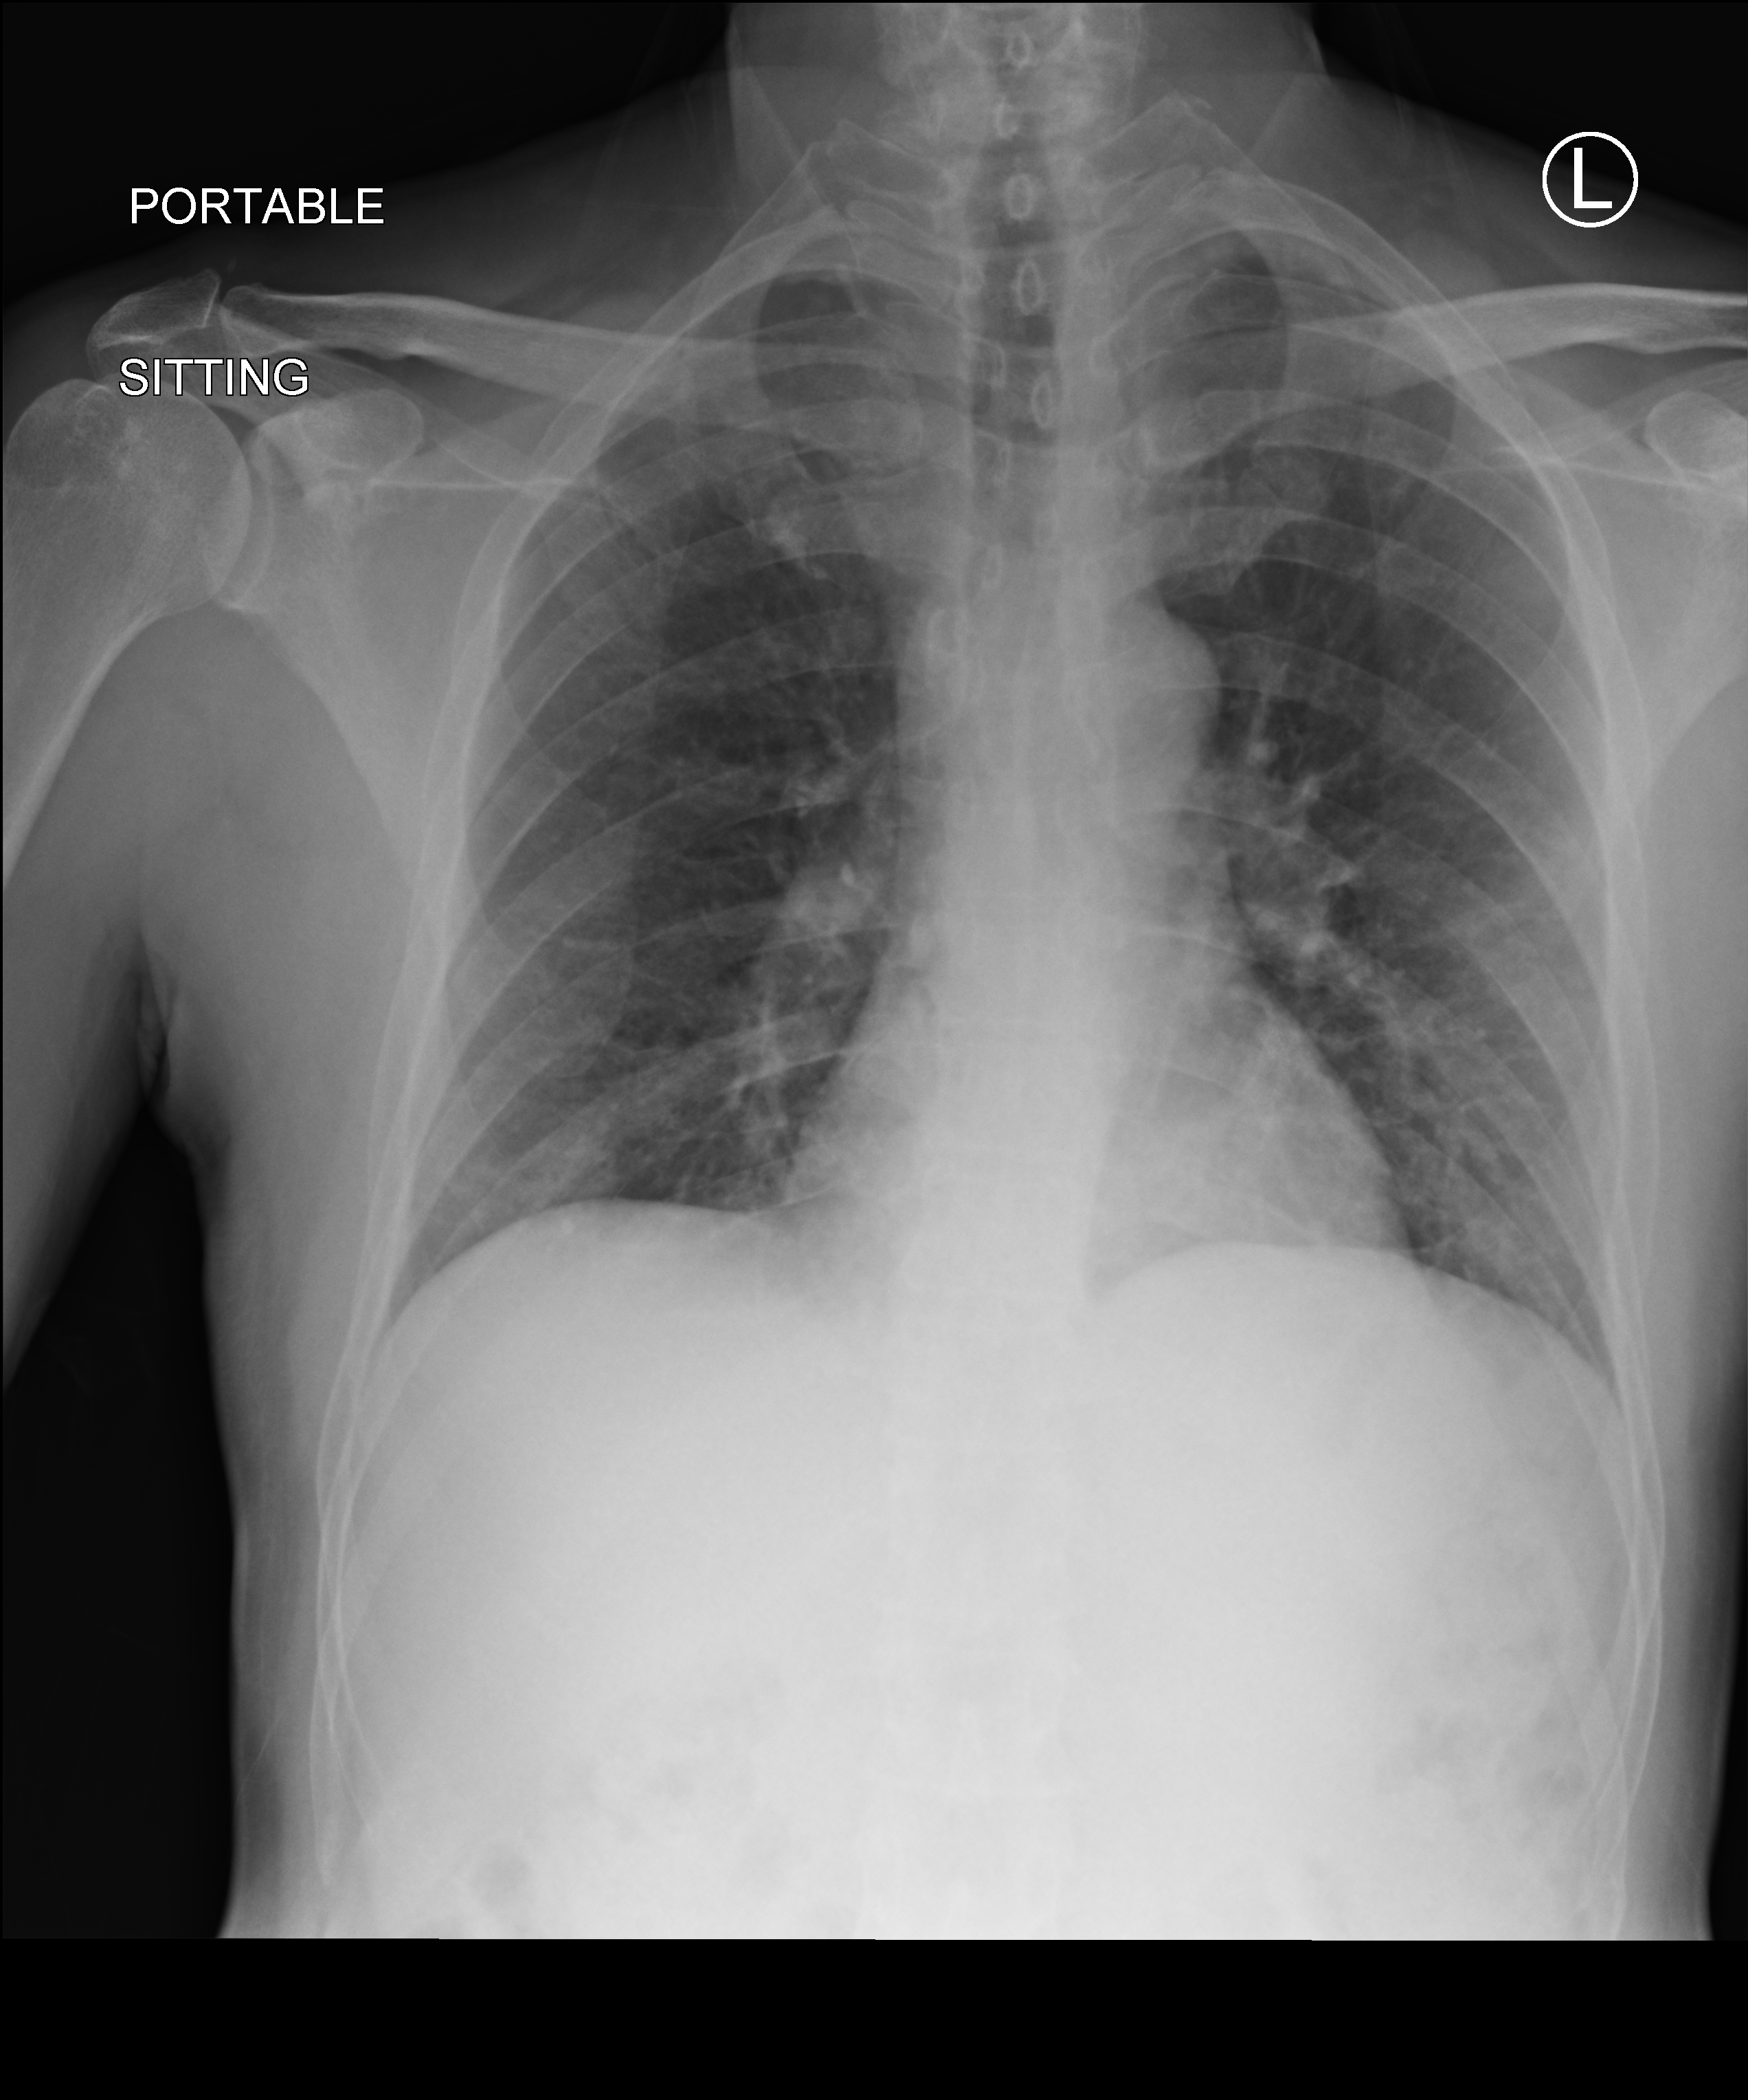
Portable chest radiograph, anteroposterior (AP) projection. Patient hospitalised with COVID-19; male, aged 60–74 years.
From the hospital-stay record, not from the radiograph (when in the stay this image was taken is not recorded):
- mechanically ventilated during this hospital stay: no
- admitted to intensive care during this hospital stay: no